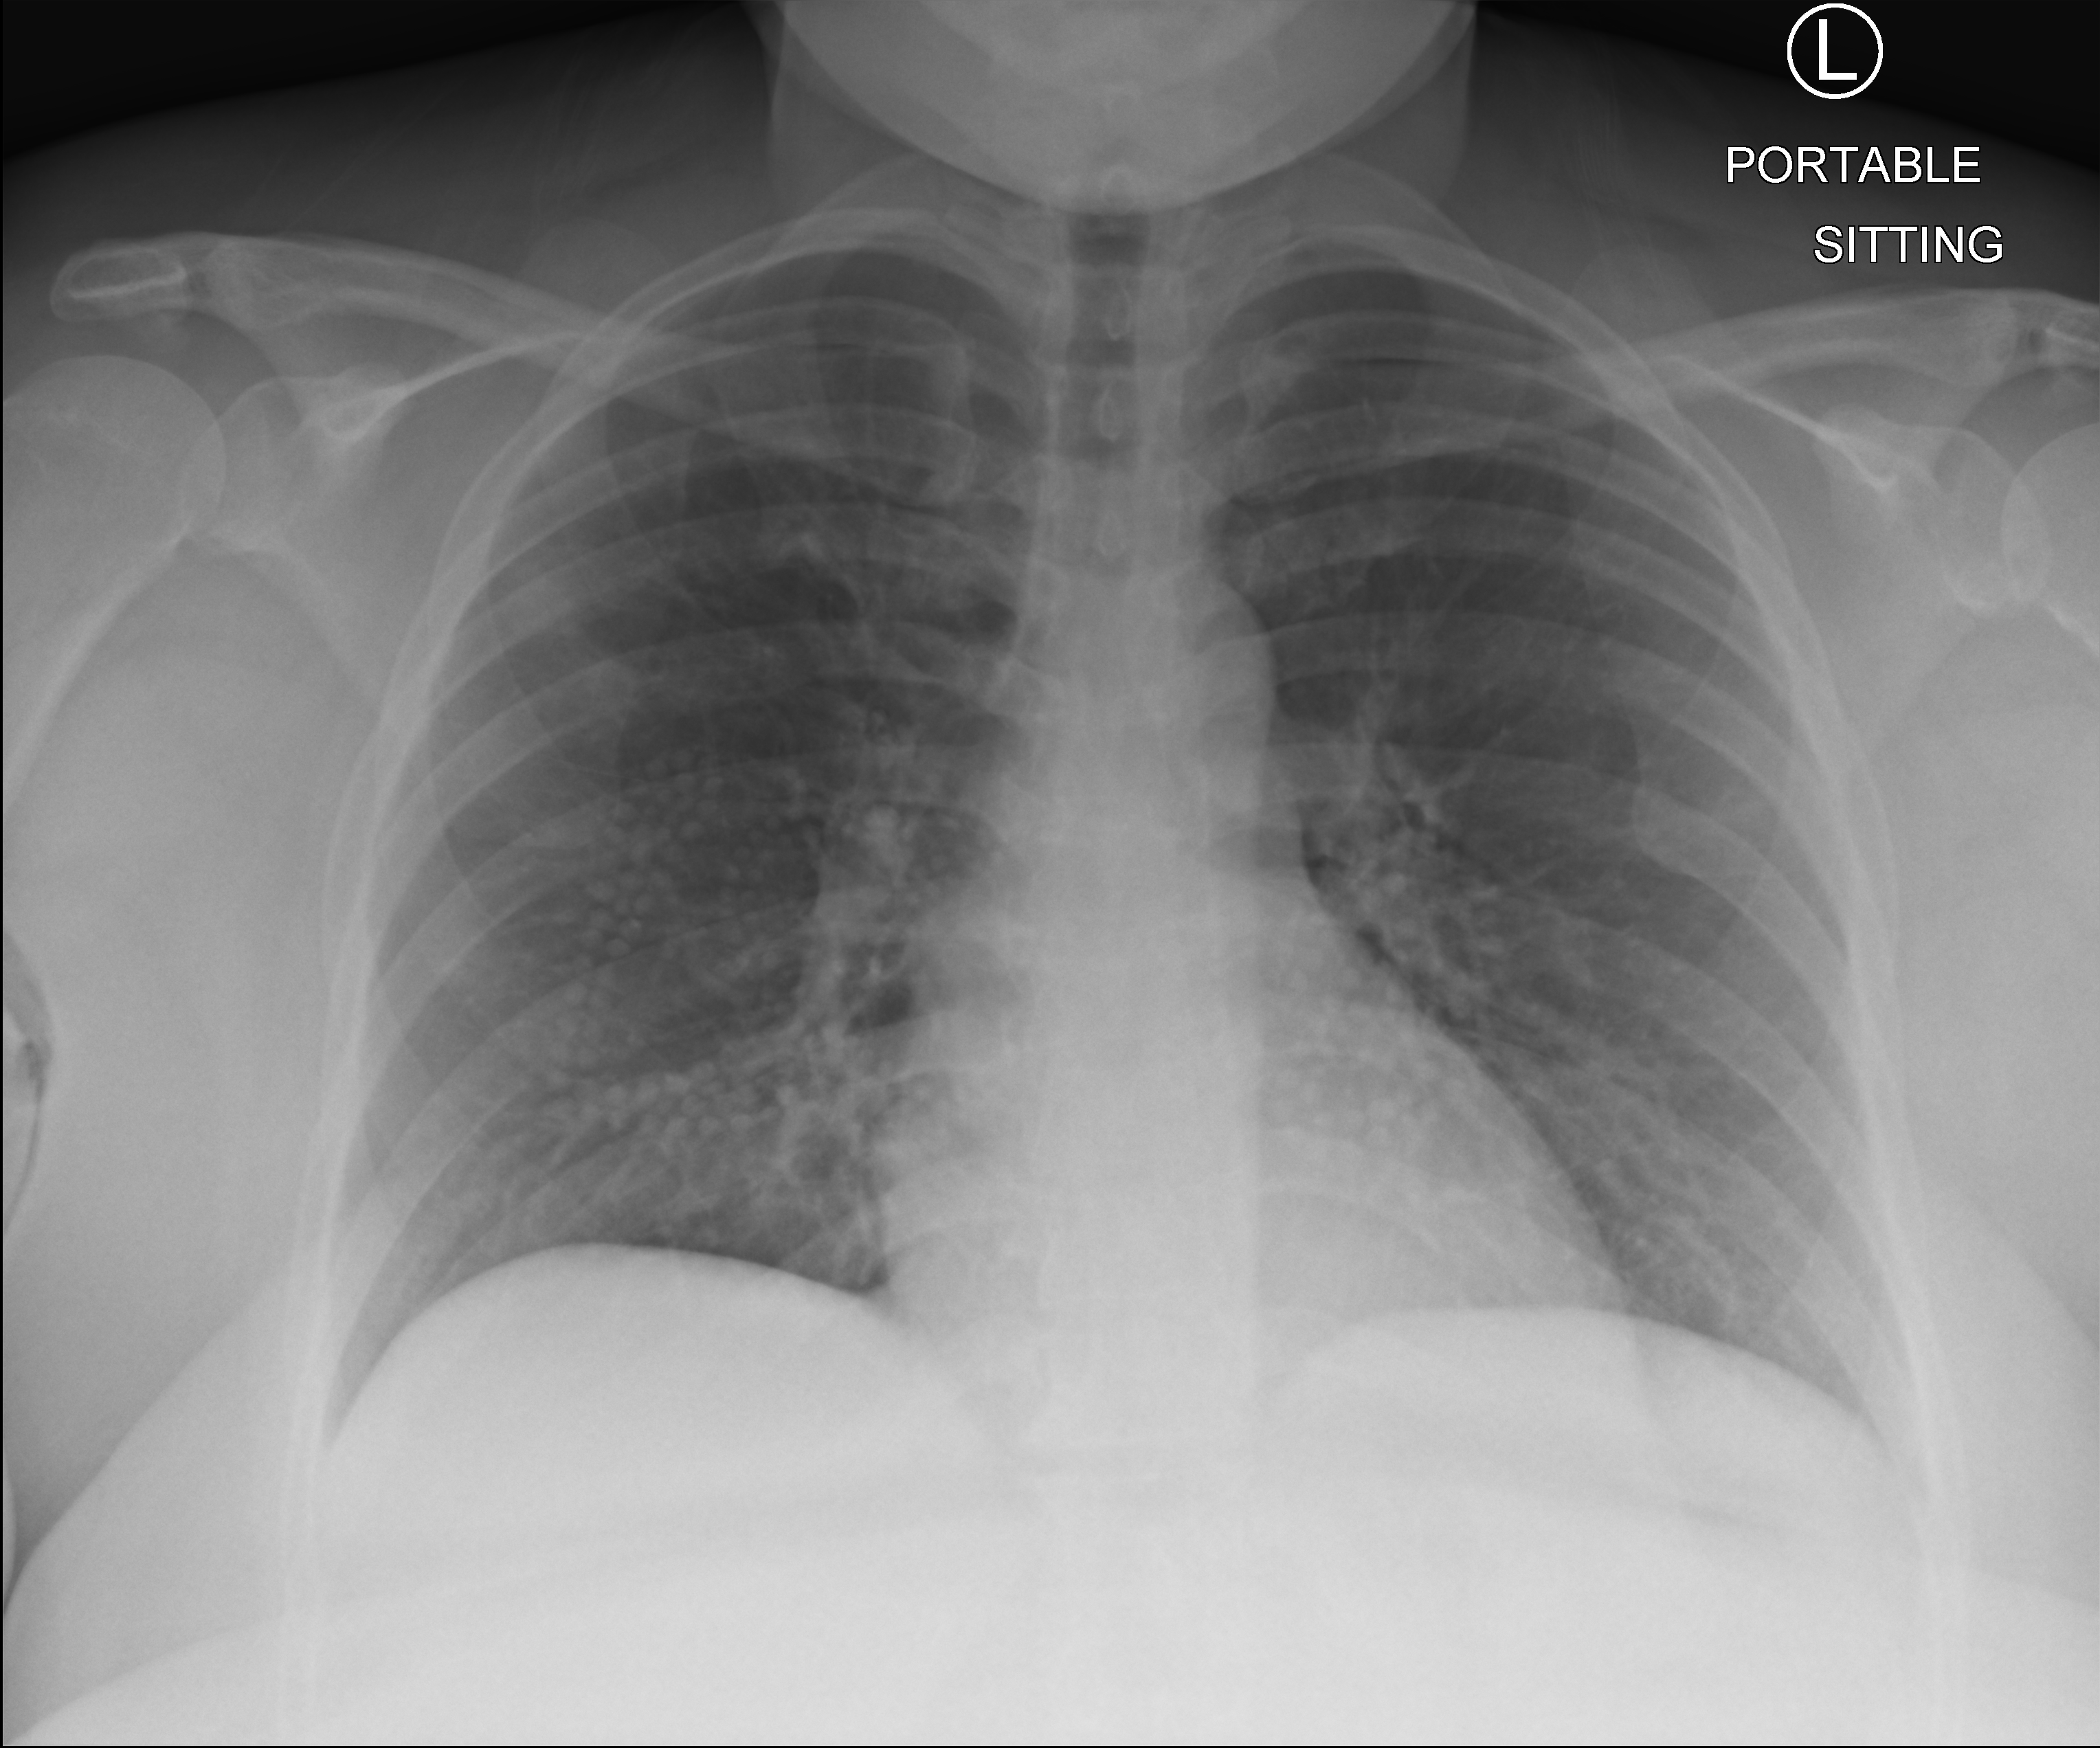
Bedside chest radiograph (computed radiography), anteroposterior (AP) projection. Patient hospitalised with COVID-19; female, aged 18–59 years.
From the hospital-stay record, not from the radiograph (when in the stay this image was taken is not recorded):
- admitted to intensive care during this hospital stay: no